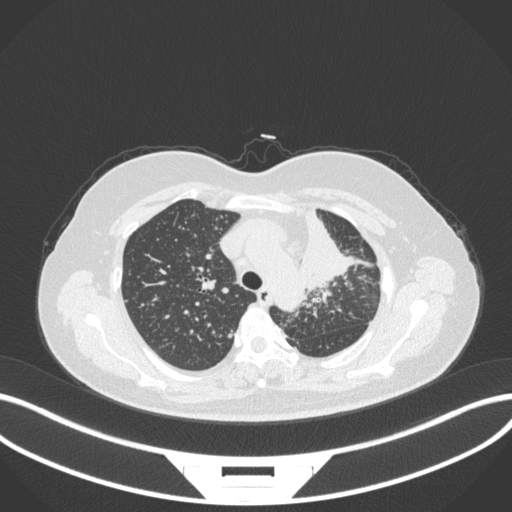
Chest CT, one axial slice. Position 251 of 348 along the scan axis. Reconstruction kernel B31f. 120 kVp. Lung window (W 1500 / L -600 HU). 512 × 512 image matrix, field of view 400 × 400 mm. Female patient, age 49 years. From the clinical record (not read from this slice): clinical TNM (as recorded): T1c N0 M1.
Structures marked on this image (rectangle marked by the reading radiologist):
- lung tumour (recorded histology: adenocarcinoma): box from (x=294, y=197) to (x=353, y=292) px